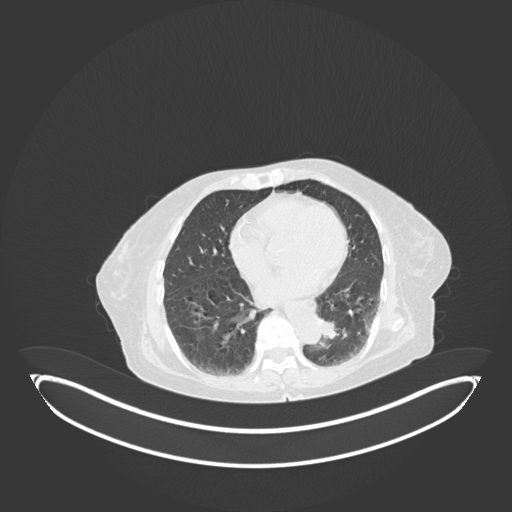
Chest CT, one axial slice; position 33 of 189 along the scan axis; lung window (W 1500 / L -600 HU); 1 mm slice thickness; 512 × 512 image matrix, field of view 500 × 500 mm. Patient: female, 82 years. Case-level facts recorded for this patient, not image findings: clinical TNM (as recorded): T1b N0 M1.
Annotated regions visible in this slice (rectangle marked by the reading radiologist):
- lung tumour (recorded histology: adenocarcinoma): bounding box [x1, y1, x2, y2] px = [317, 314, 341, 347]